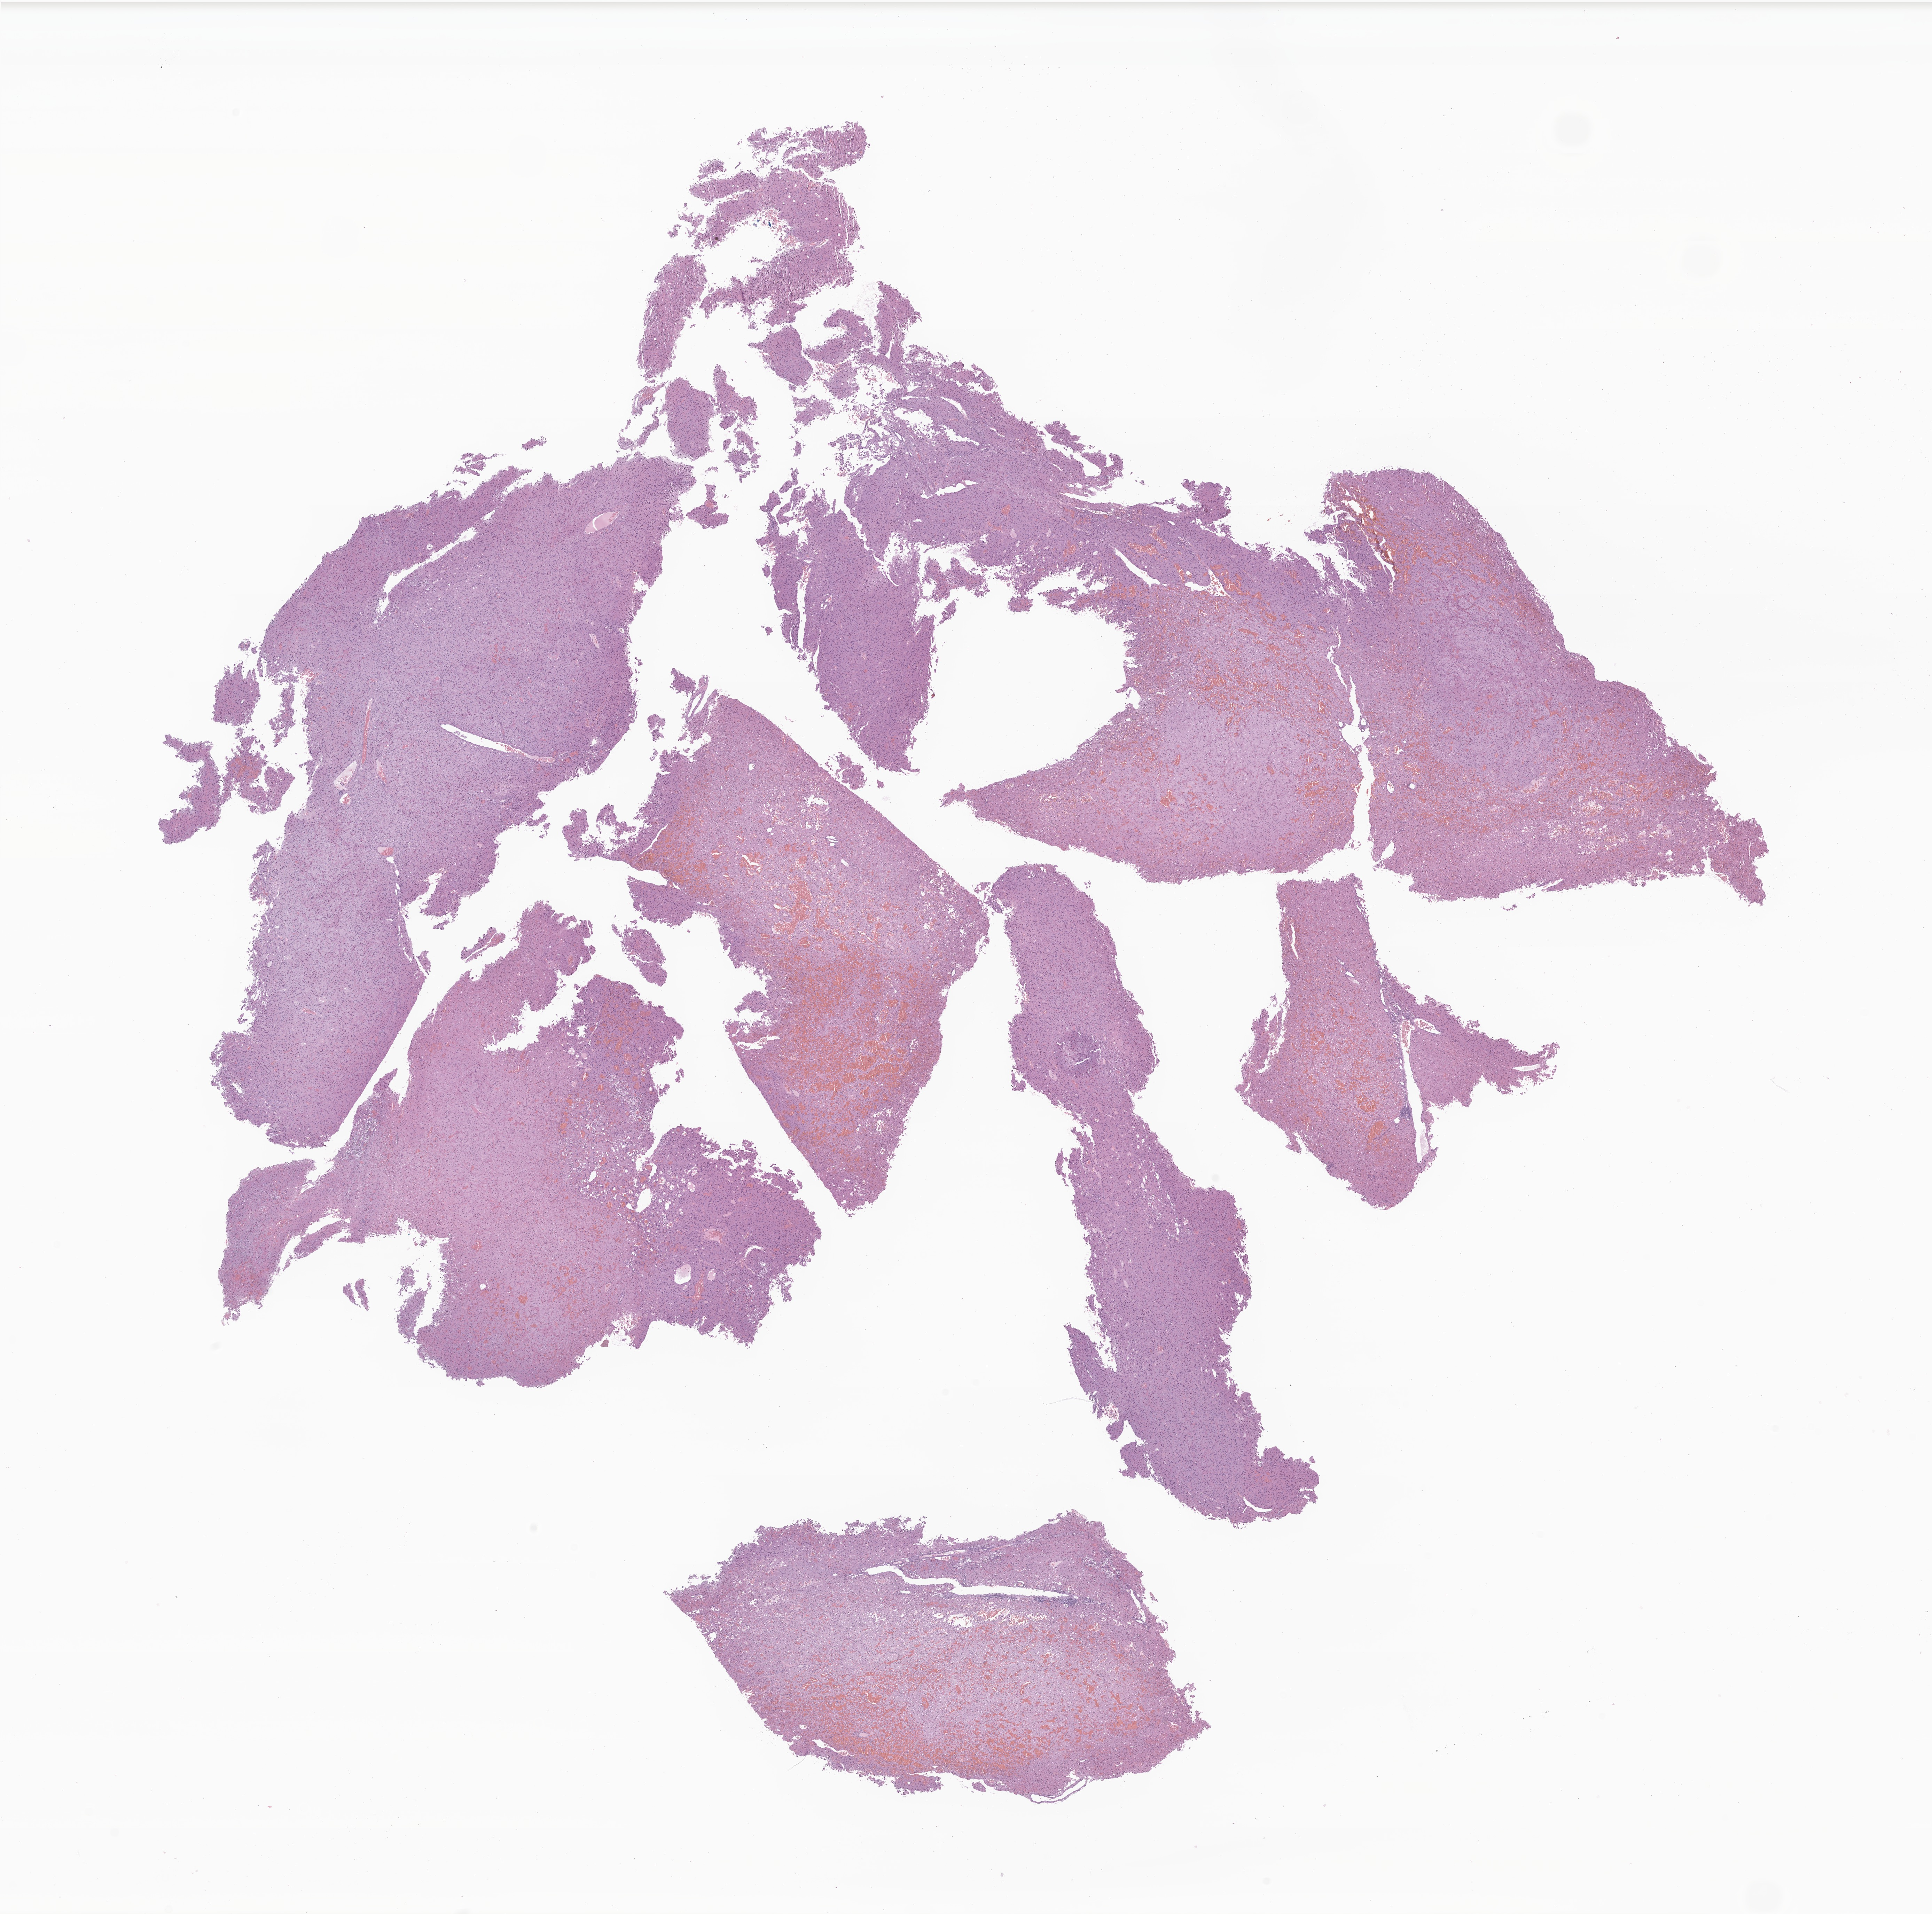
Whole-slide image, haematoxylin and eosin stain of tumor tissue from the adrenal gland, shown as a low-resolution overview of the whole scanned area (about 23.4 x 23.2 mm). Formalin-fixed, paraffin-embedded (FFPE) tissue. Female patient, age 80 months (6 years 8 months).
* recorded diagnosis: Adrenal cortical carcinoma